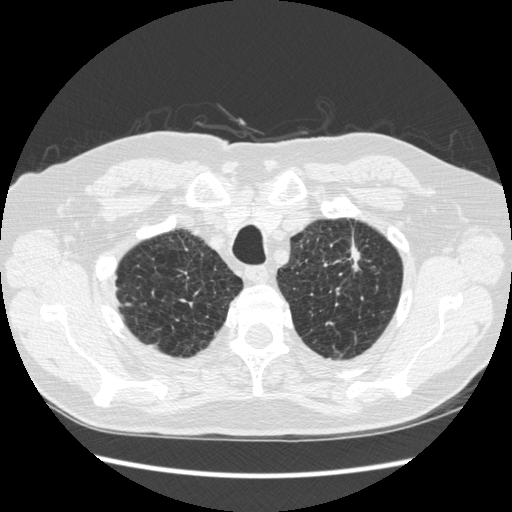
Low-dose screening chest CT, one axial slice. Position 232 of 267 along the scan axis. Reconstruction kernel STANDARD. 120 kVp. Lung window (W 1500 / L -600 HU). 512 × 512 image matrix, field of view 360 × 360 mm.
Structures marked on this image (manually delineated by an expert):
- lesion 1 (tumor, upper lobe of left lung): bounding box [x1, y1, x2, y2] px = [349, 242, 360, 268]